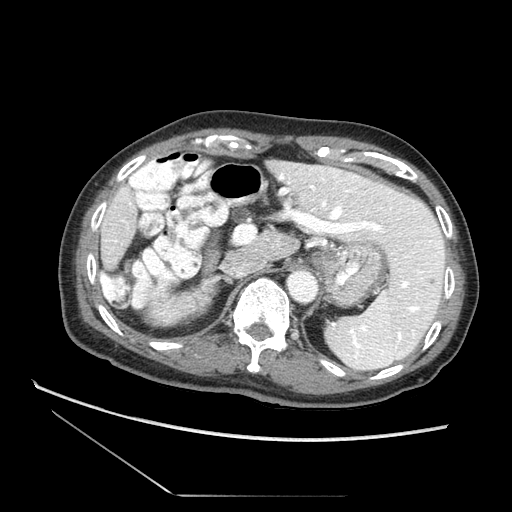
Contrast-enhanced abdominal CT (liver protocol), one axial slice. 120 kVp. Soft-tissue window (W 400 / L 40 HU). 2.5 mm slice thickness. 512 × 512 image matrix, field of view 360 × 360 mm. Case-level facts recorded for this patient, not image findings: diagnosis: hepatocellular carcinoma (patient treated with transarterial chemoembolisation; whether this scan precedes or follows treatment is not stated here); TNM stage (as recorded): Stage-II; Child-Pugh class: A; tumour differentiation: moderately differentiated; tumour nodularity: multinodular.
Structures marked on this image (semi-automatically segmented with operator editing):
- liver parenchyma outside the tumour (the mass and vessels are separate outlines, so this box may not span the whole liver): bounding box [x1, y1, x2, y2] px = [100, 160, 449, 356]
- liver vessels: [311, 185, 423, 331]